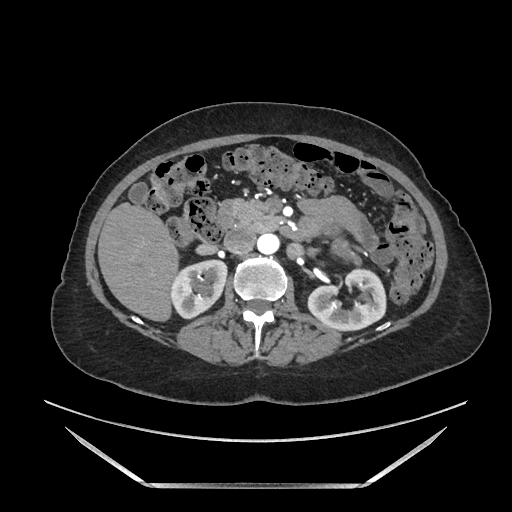
Contrast-enhanced abdominal CT, one axial slice. Soft-tissue window (W 400 / L 40 HU). 1.25 mm slice thickness. 512 × 512 image matrix, field of view 440 × 440 mm. Female patient. Case-level facts recorded for this patient, not image findings: diagnosis: adrenocortical carcinoma; tumour side: left adrenal; tumour size at pathology: 12.5 cm; Ki-67 index: 39 %; stage (as recorded): 3.
Outlined on this slice (semi-automatic segmentation, software-assisted and operator-edited):
- mass: box from (x=334, y=235) to (x=360, y=265) px